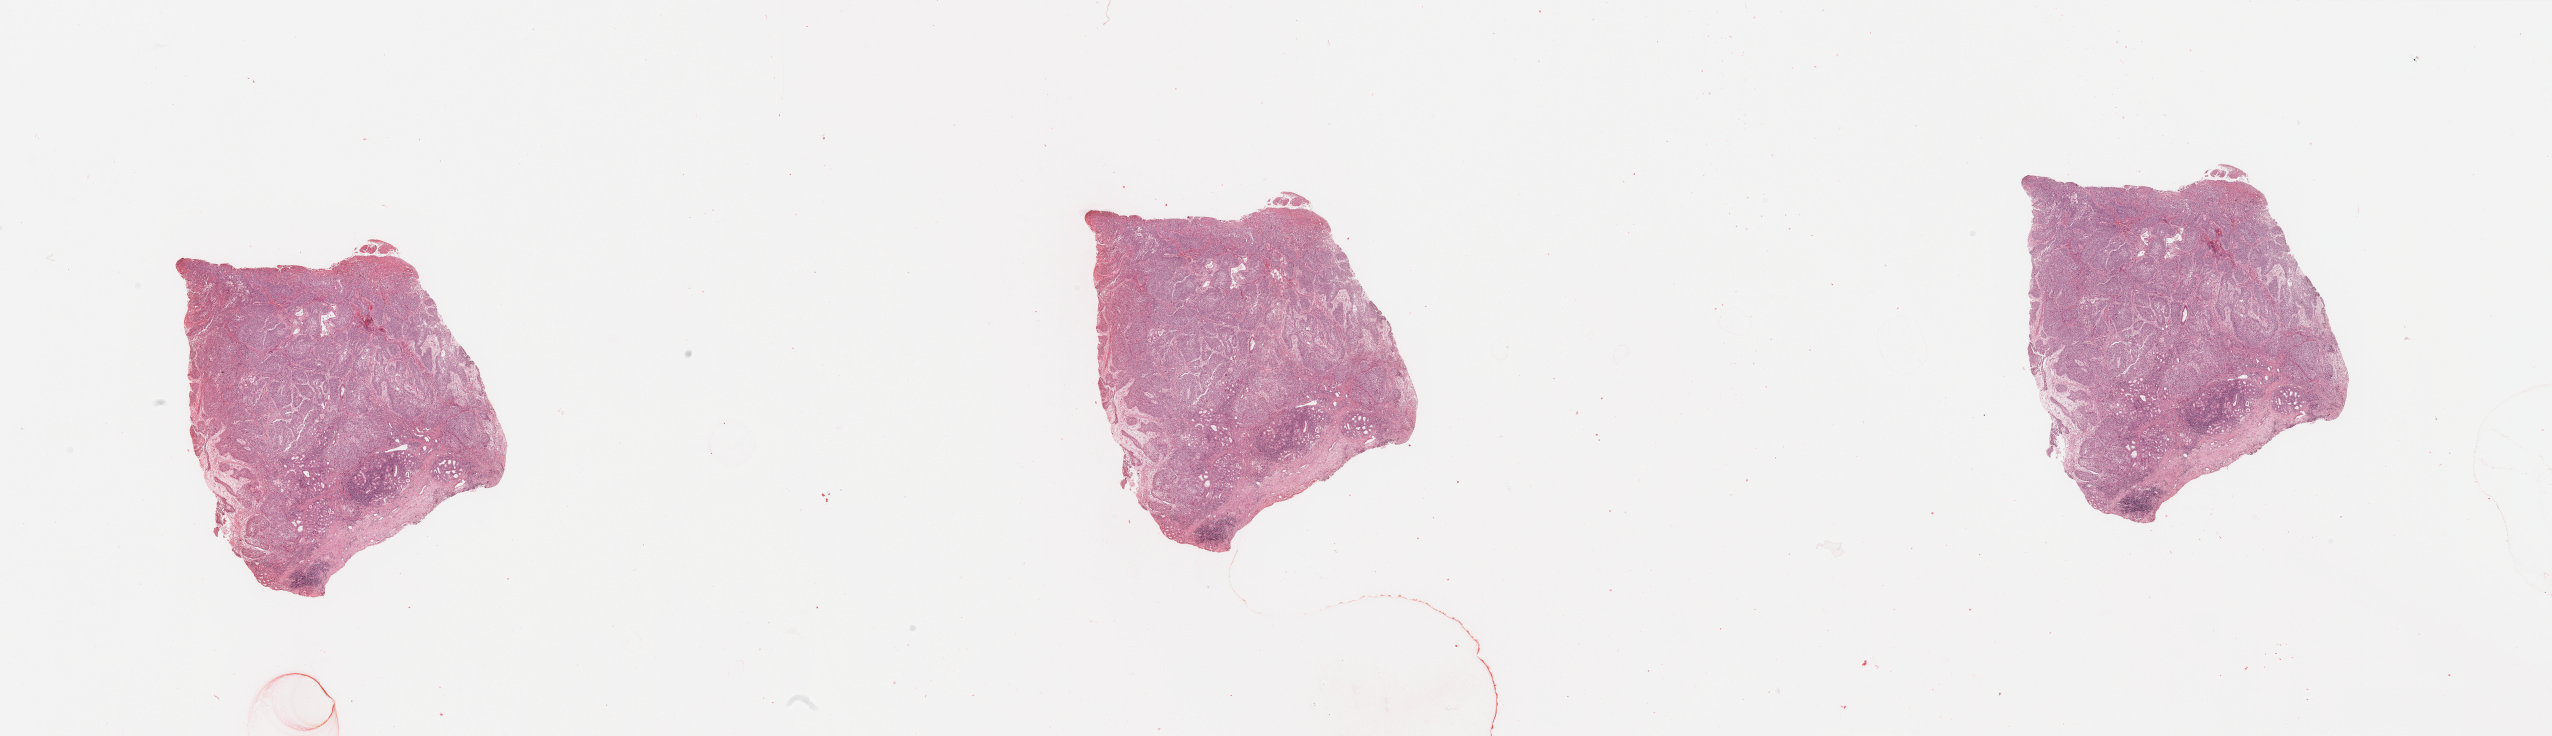
Whole-slide histology image, H&E — shown as a low-resolution overview of the whole scanned area (about 40.4 x 11.6 mm, acquisition: 20x scan), head and neck, tissue type not recorded. Patient: male, age 60 years.
* patient diagnosis: Squamous cell carcinoma, NOS (larynx, NOS)